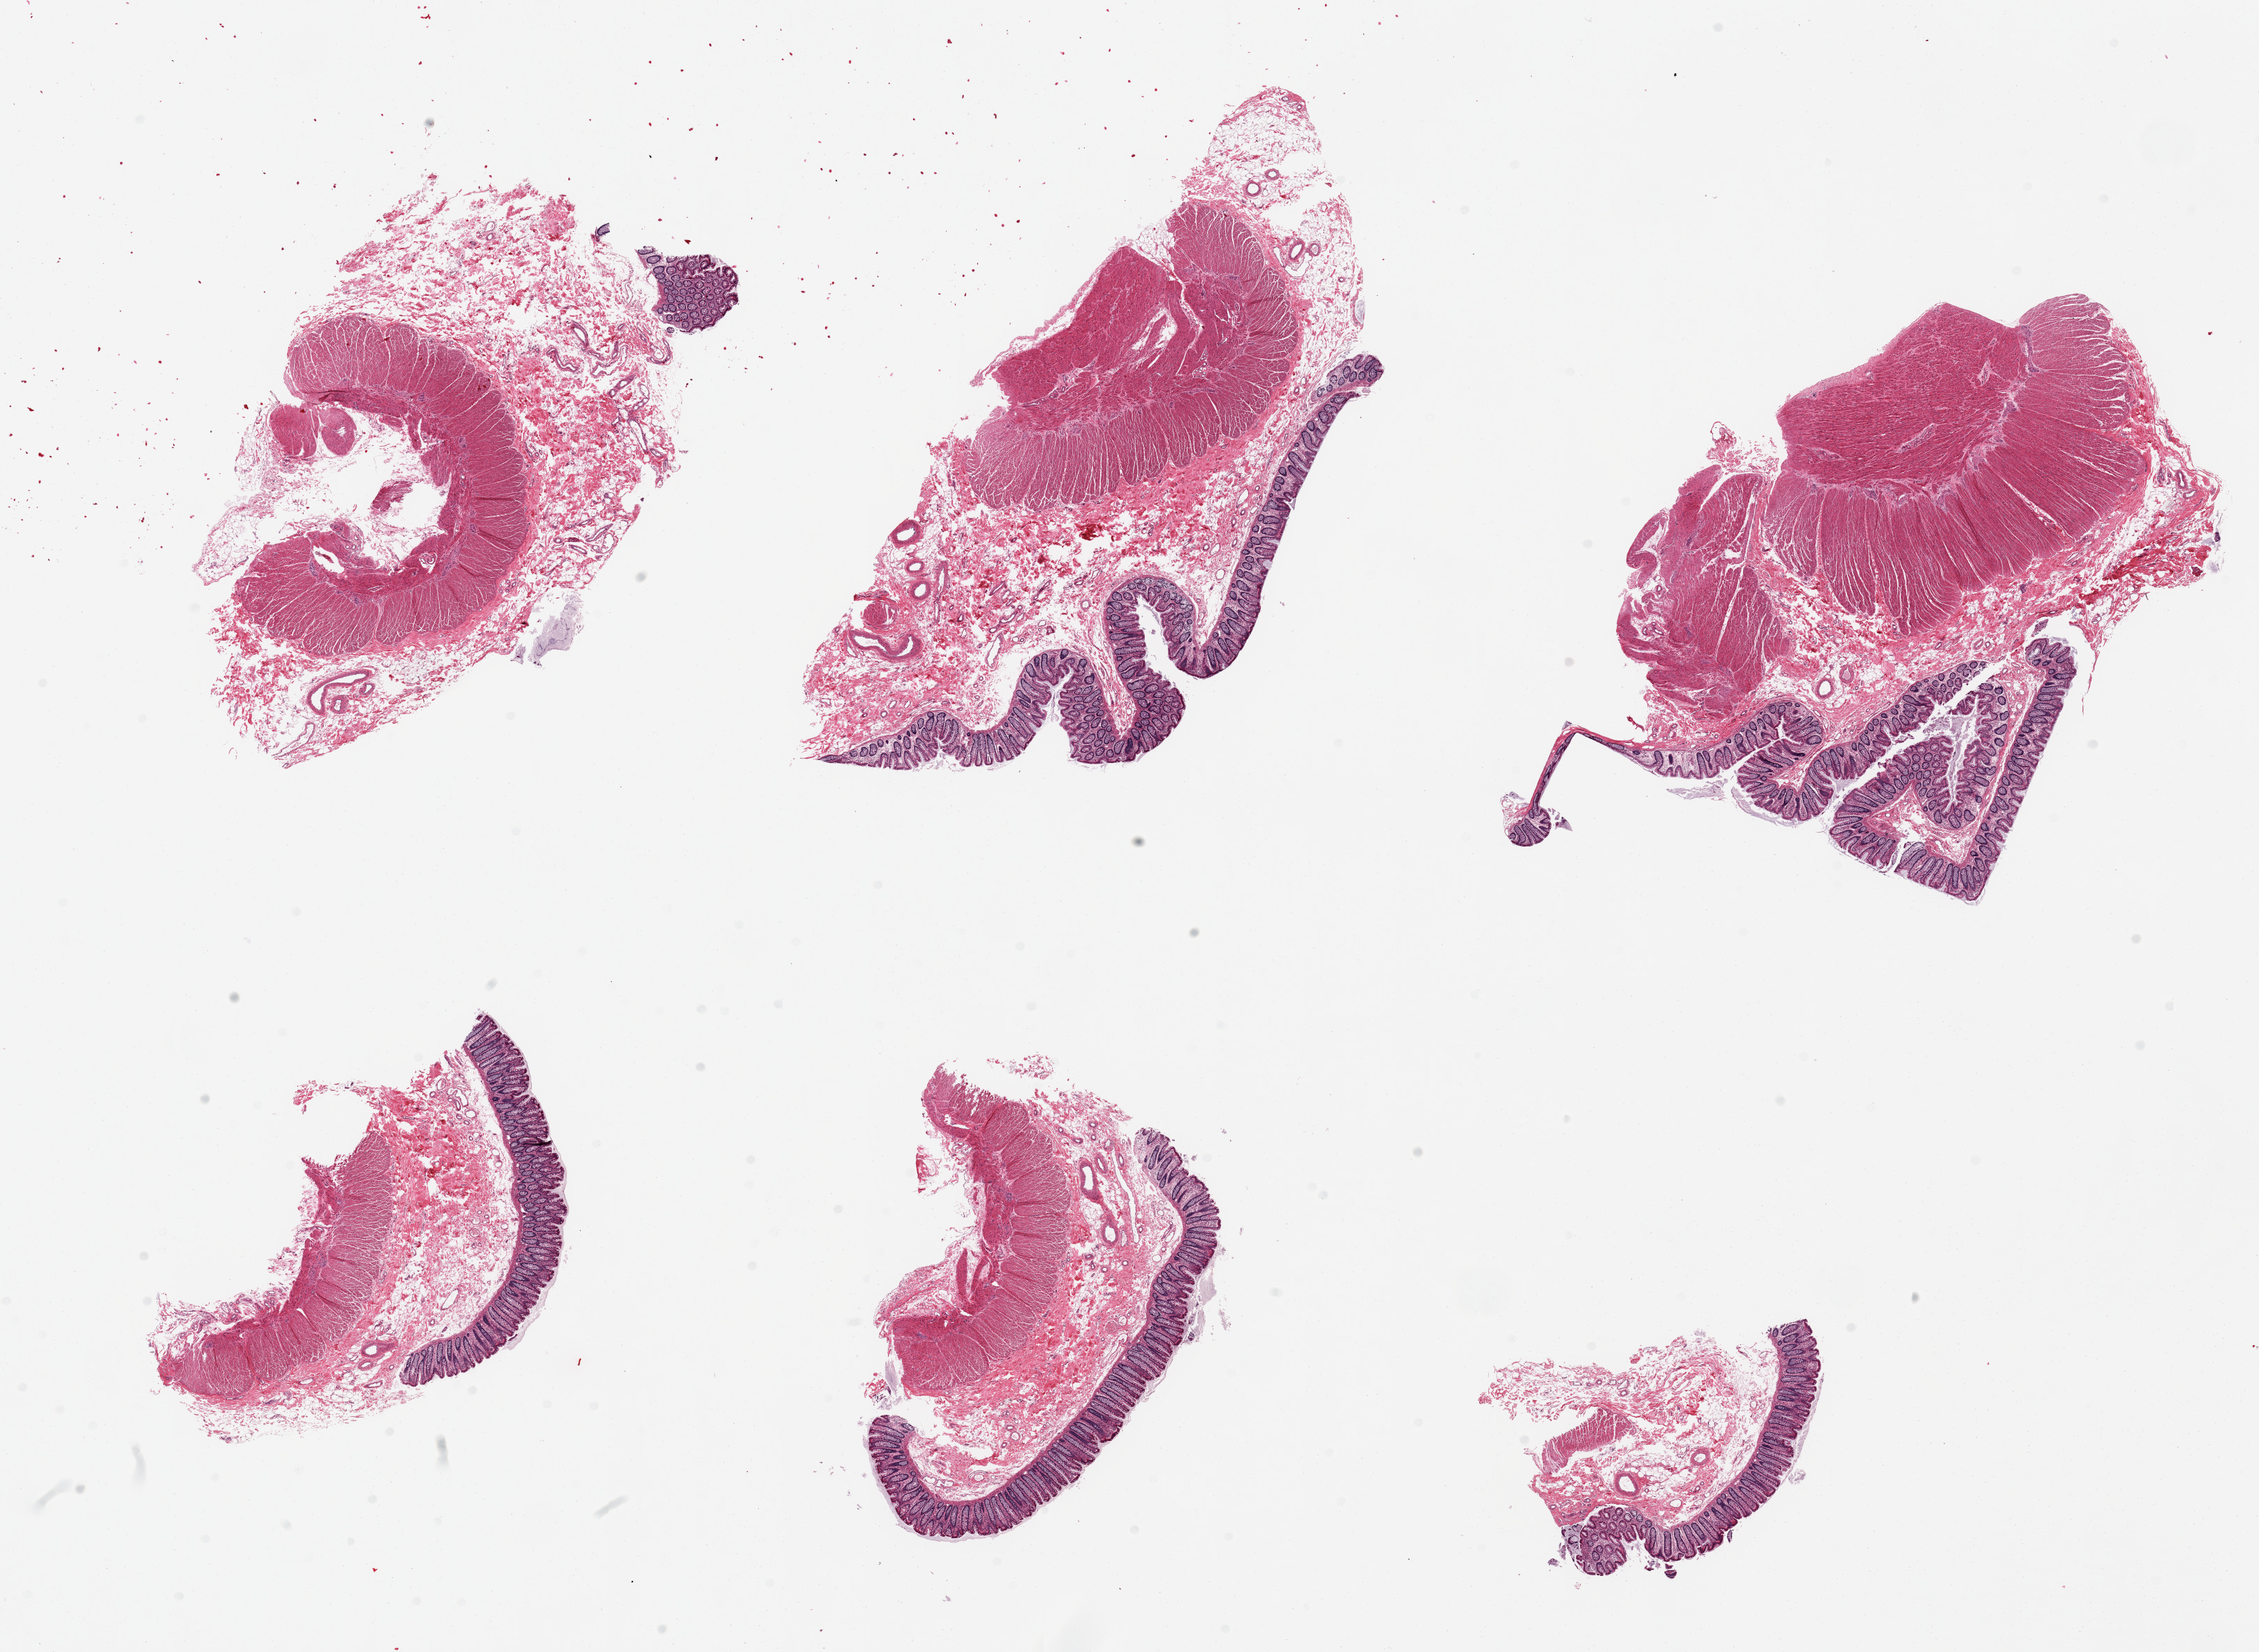
Digitized hematoxylin and eosin (H&E)-stained section, shown as a low-resolution overview of the whole scanned area (about 25.6 x 18.7 mm, from a 20x scan); PAXgene-fixed paraffin-embedded (PFPE) section; target tissue: transverse colon; tissue donor sample. Donor sex: male.
- reviewer comment on this tissue sample: 6 pieces, mucosa ~0.3mm, ~5-10% thickness